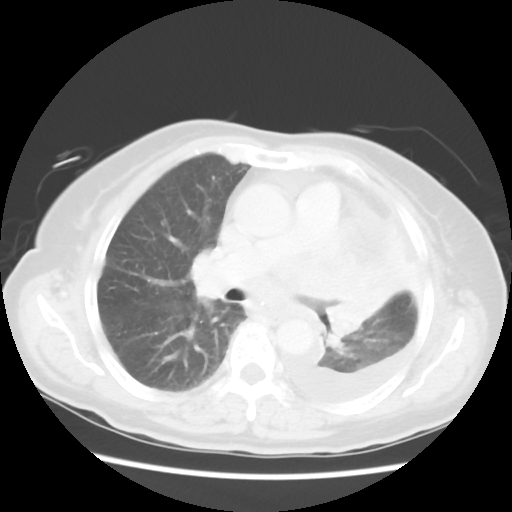
Chest CT, one axial slice; position 32 of 52 along the scan axis; 120 kVp; lung window (W 1500 / L -600 HU); 5 mm slice thickness; 512 × 512 image matrix, field of view 336 × 336 mm. Patient: female, 72 years. From the clinical record (not read from this slice): clinical TNM (as recorded): T4 N3 M1b.
Outlined on this slice (rectangle marked by the reading radiologist):
- lung tumour (recorded histology: large cell carcinoma): box from (x=303, y=245) to (x=390, y=345) px